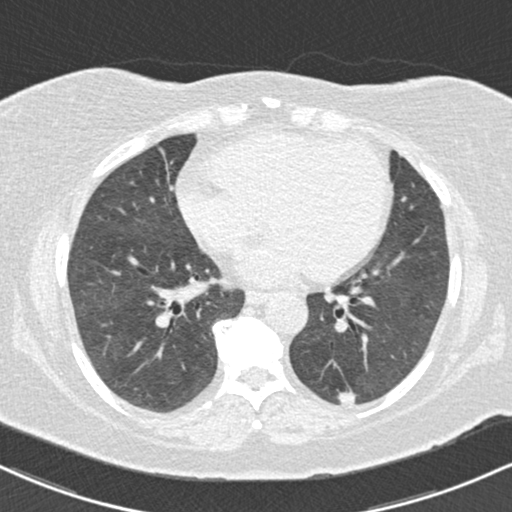
Low-dose screening chest CT, one axial slice. Reconstruction kernel B30f. 120 kVp. Lung window (W 1500 / L -600 HU). 2 mm slice thickness. 512 × 512 image matrix.
Annotated regions visible in this slice (manually delineated by an expert):
- lesion 1 (tumor, lower lobe of left lung): bounding box [x1, y1, x2, y2] px = [337, 390, 356, 405]